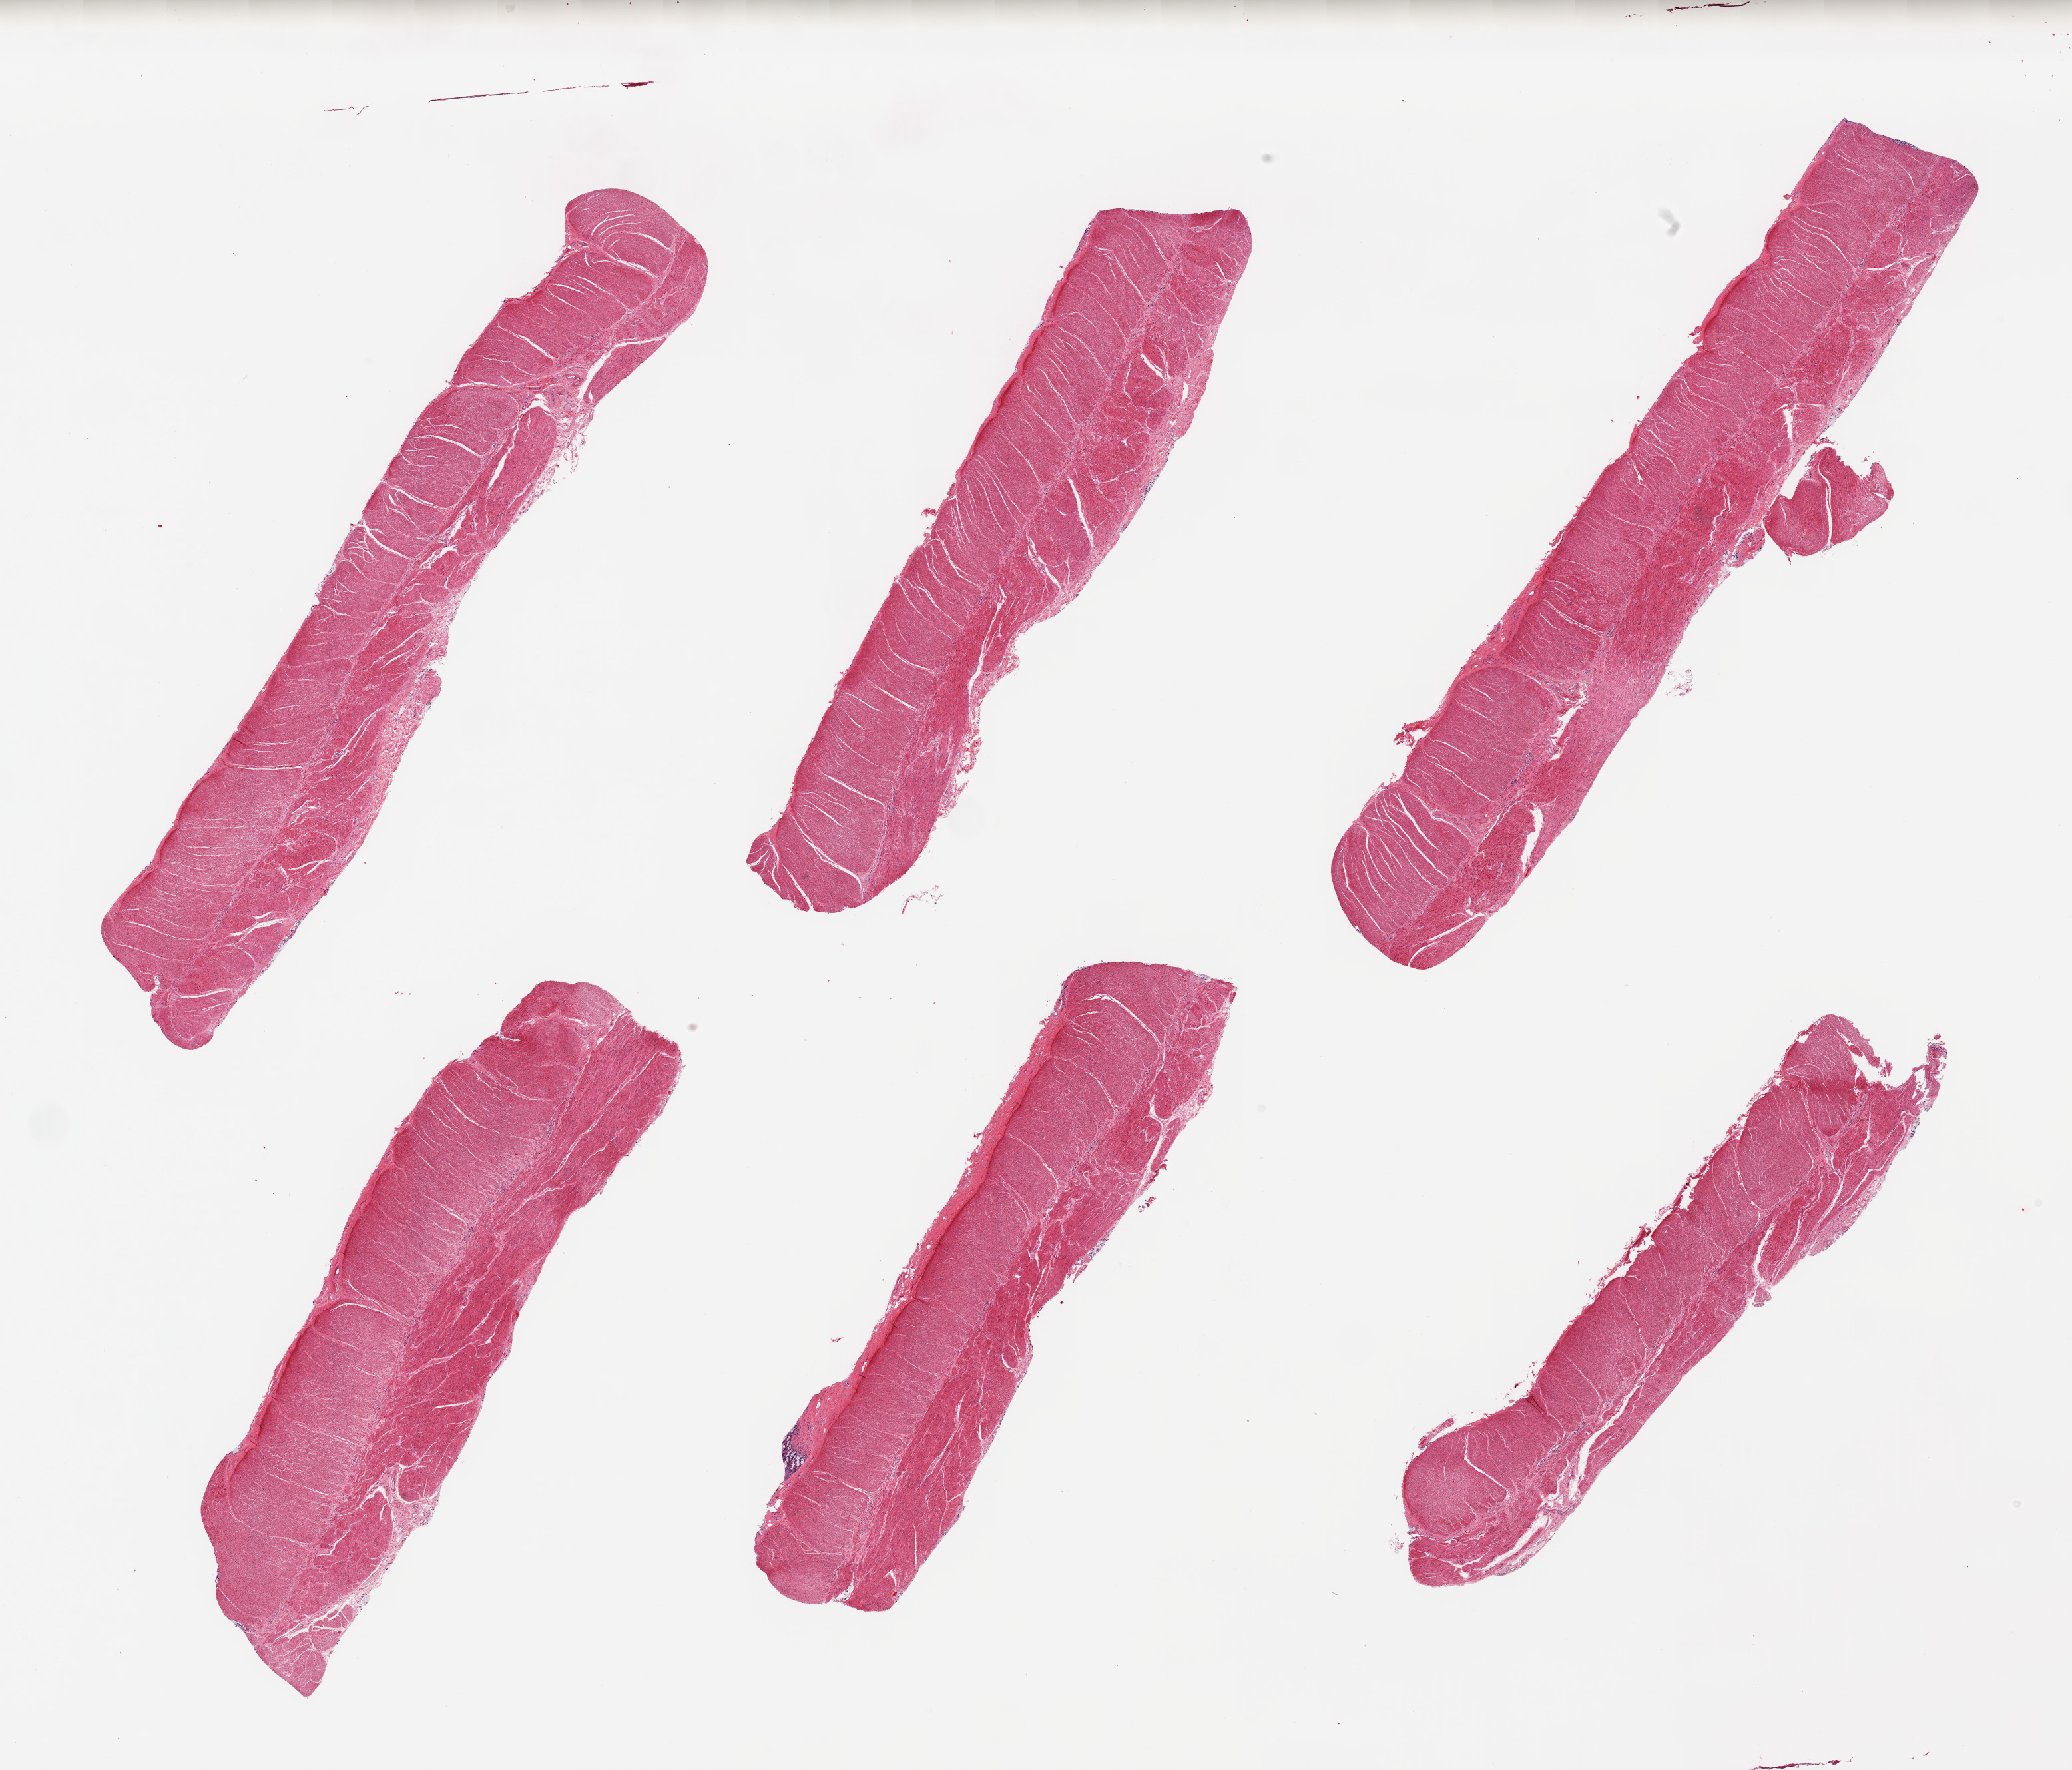
Whole-slide image, H&E stain — shown as a low-resolution overview of the whole scanned area (about 24.6 x 21.0 mm, from a 20x scan), PAXgene-fixed paraffin-embedded (PFPE) section, sampled site (target tissue): sigmoid colon, donor tissue sample. Female donor.
Review note (as recorded): 6 pieces; well dissected muscularis.